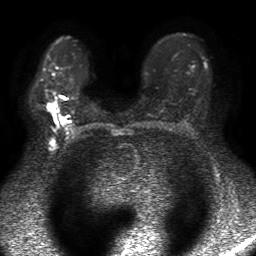
Breast MRI, one axial slice. Slice 34 of 50 in the series (ordered by position). Diffusion-weighted series; image 2 of 4 stored at this slice position (different b-values; order by instance number). 1.5 T. 4 mm slice thickness. 256 × 256 image matrix. Female patient.
Structures marked on this image (manually delineated by an expert):
- tumour on diffusion-weighted imaging: bounding box (x1, y1, x2, y2) in pixels: (47, 102, 54, 111)